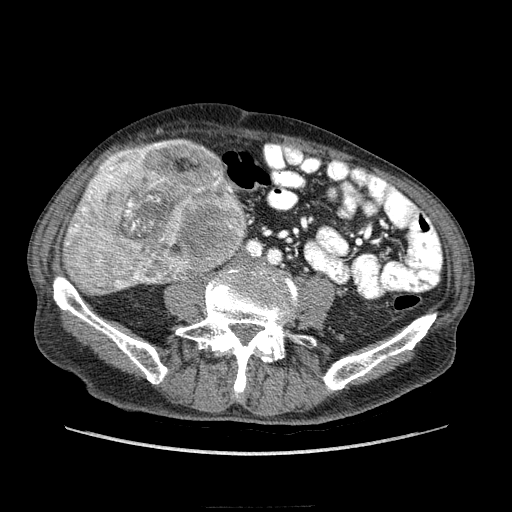
Contrast-enhanced abdominal CT (liver protocol), one axial slice. Position 41 of 218 along the scan axis. Reconstruction kernel STANDARD. Soft-tissue window (W 400 / L 40 HU). 2.5 mm slice thickness. 512 × 512 image matrix, field of view 380 × 380 mm. Case-level facts recorded for this patient, not image findings: diagnosis: hepatocellular carcinoma (patient treated with transarterial chemoembolisation; whether this scan precedes or follows treatment is not stated here); TNM stage (as recorded): Stage-IIIA.
Outlined on this slice (semi-automatically segmented with operator editing):
- liver parenchyma outside the tumour (the mass and vessels are separate outlines, so this box may not span the whole liver): bounding box (x1, y1, x2, y2) in pixels: (64, 162, 148, 284)
- mass: (63, 139, 246, 295)